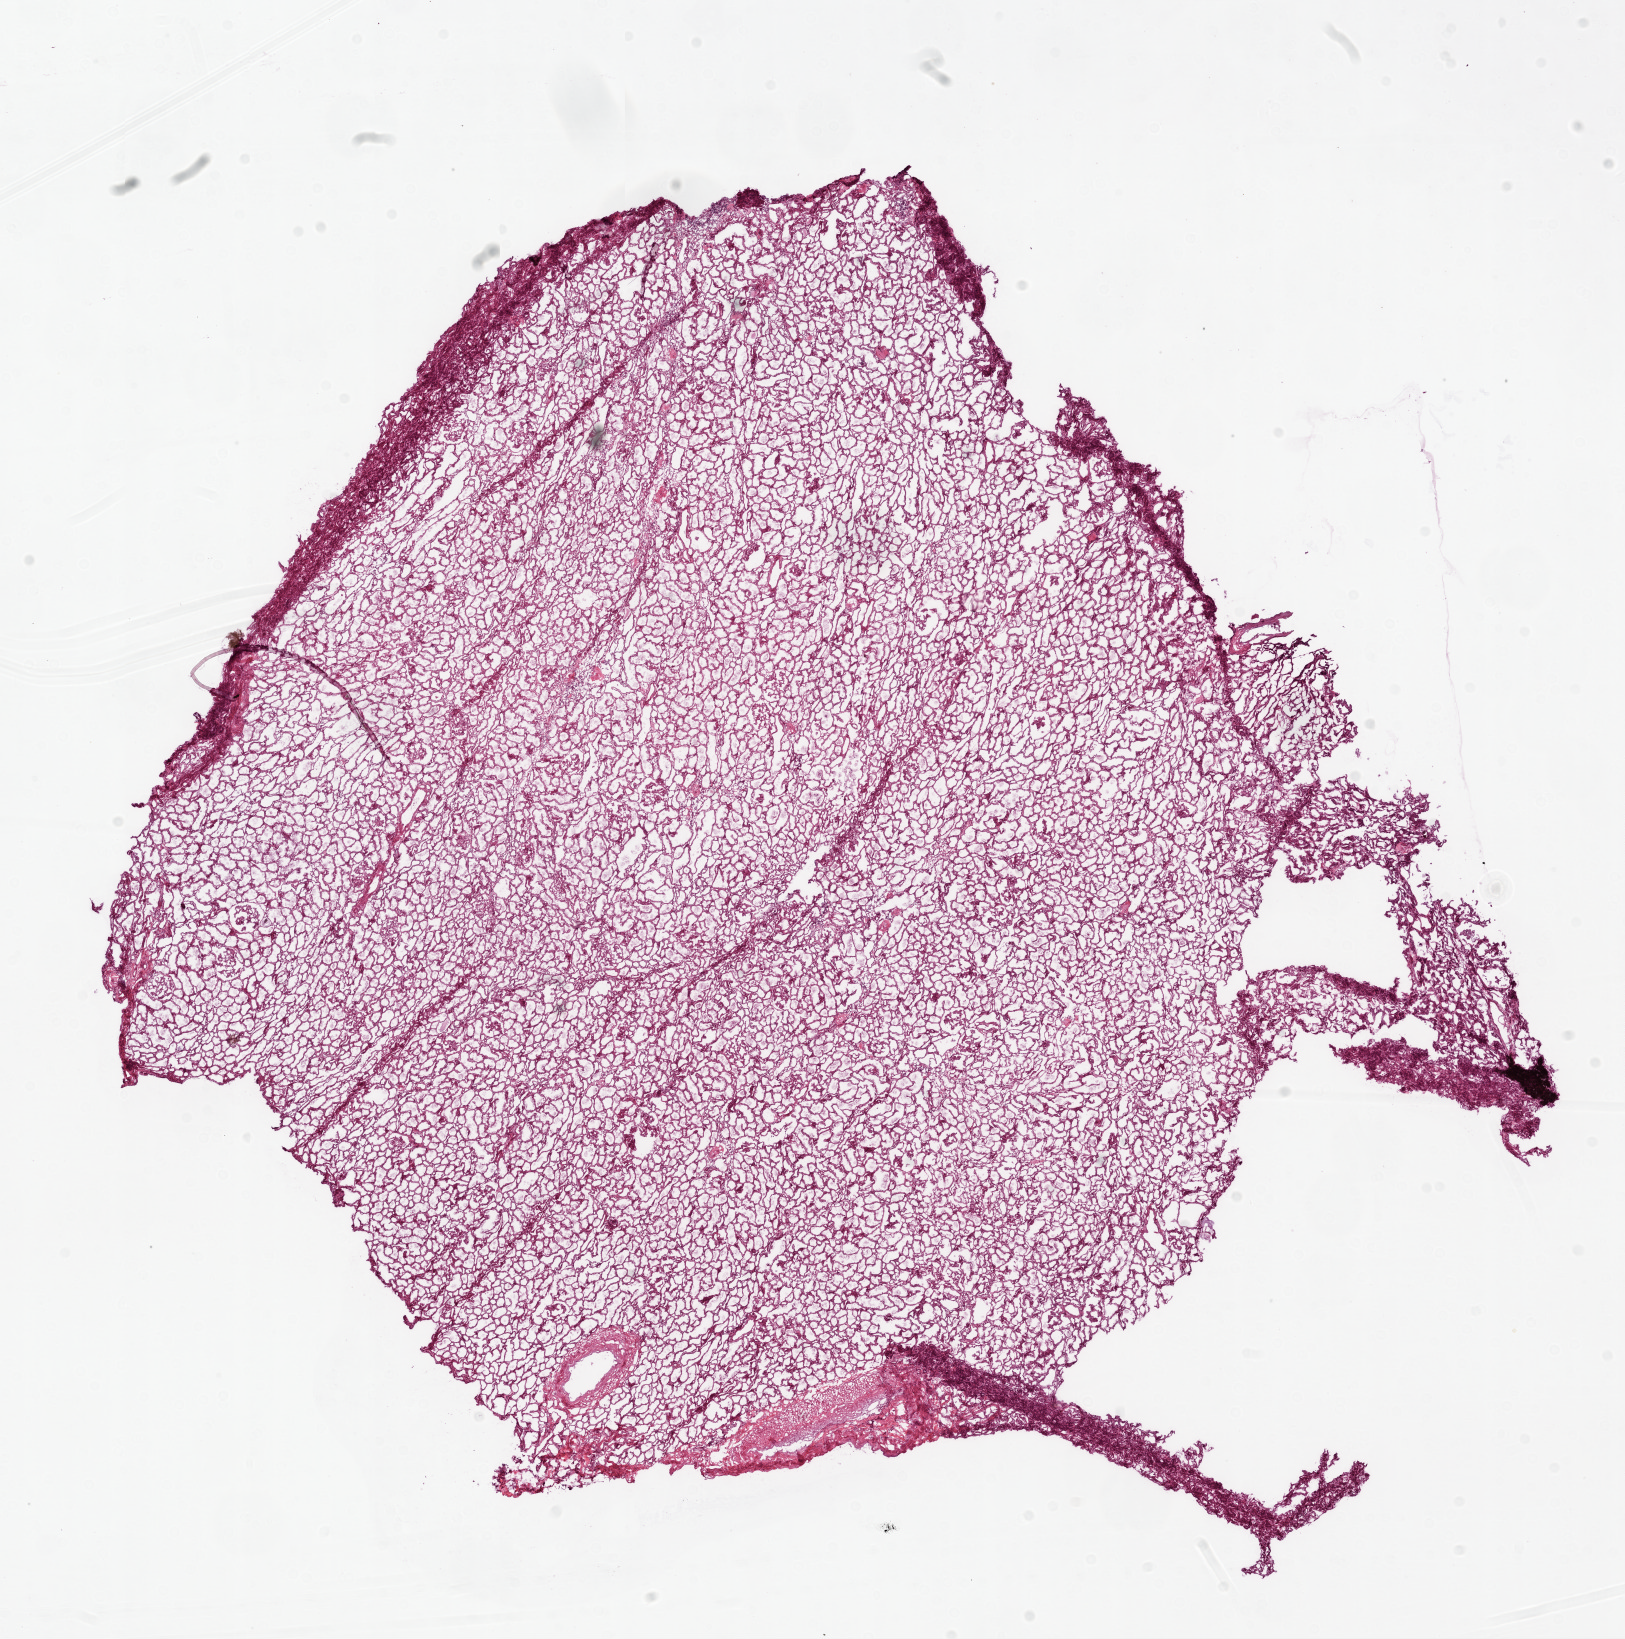
Whole-slide histology image, Hematoxylin and eosin (H&E) stained — a low-resolution overview of the entire scanned area, about 13.0 x 13.2 mm (slide scanned at 20x), frozen section, solid tissue normal (non-tumour tissue) sample from the ovary. Female patient; age at initial diagnosis 71 years.
This section: solid tissue normal (non-tumour) sample from the same patient. Patient diagnosis: Serous cystadenocarcinoma, NOS.